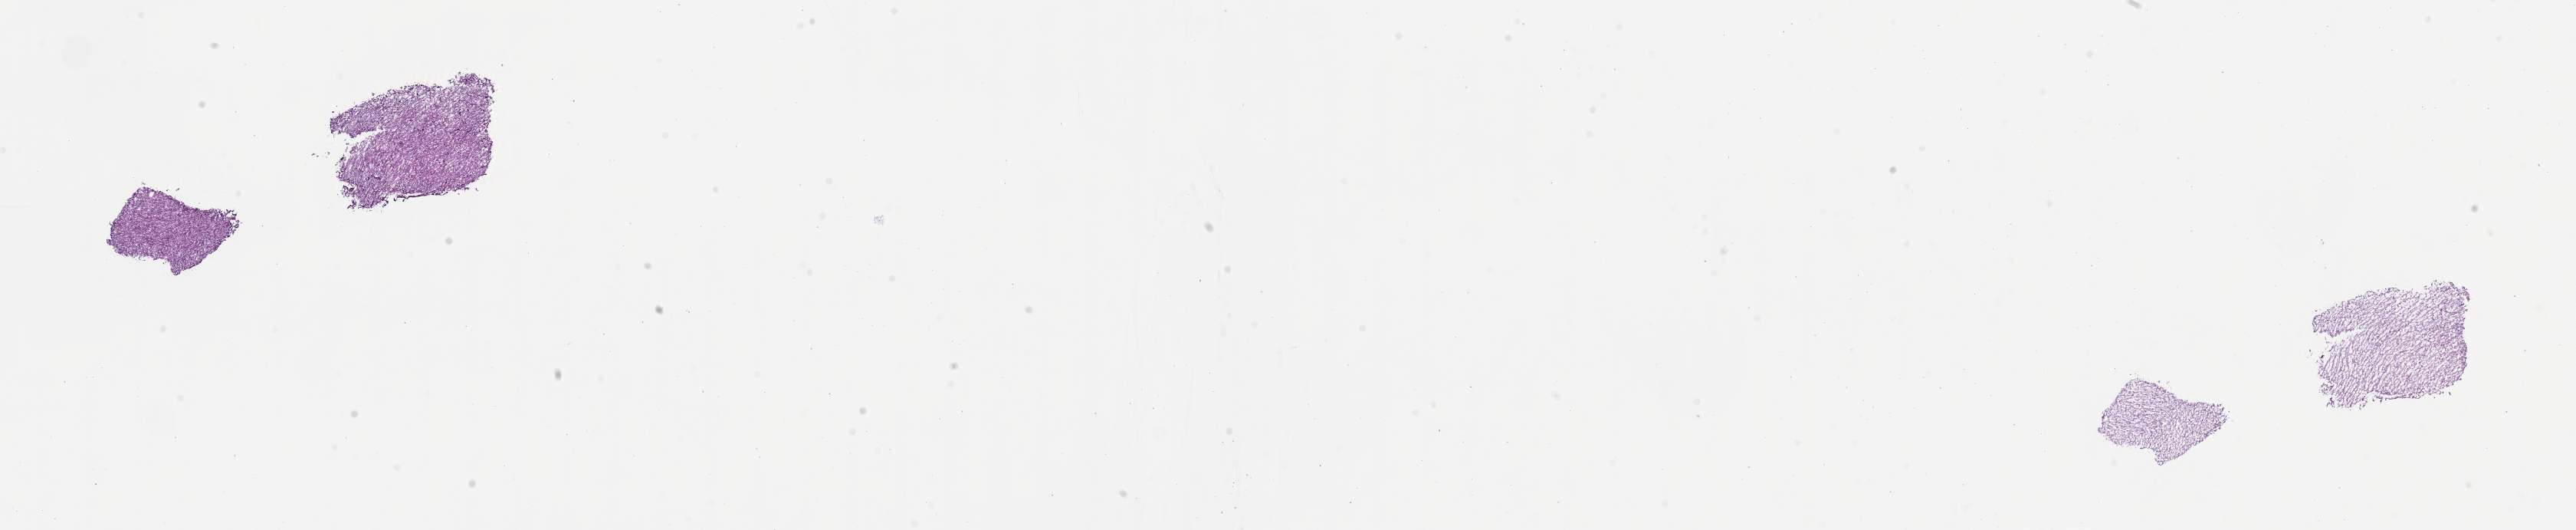
Whole-slide image, haematoxylin and eosin stain of tumor tissue from the brain, shown as a low-resolution overview of the whole scanned area (about 27.2 x 5.6 mm). Frozen section (OCT-embedded). Male patient, age 137 months (11 years 5 months).
Diagnosis: Pleomorphic xanthoastrocytoma, NOS.